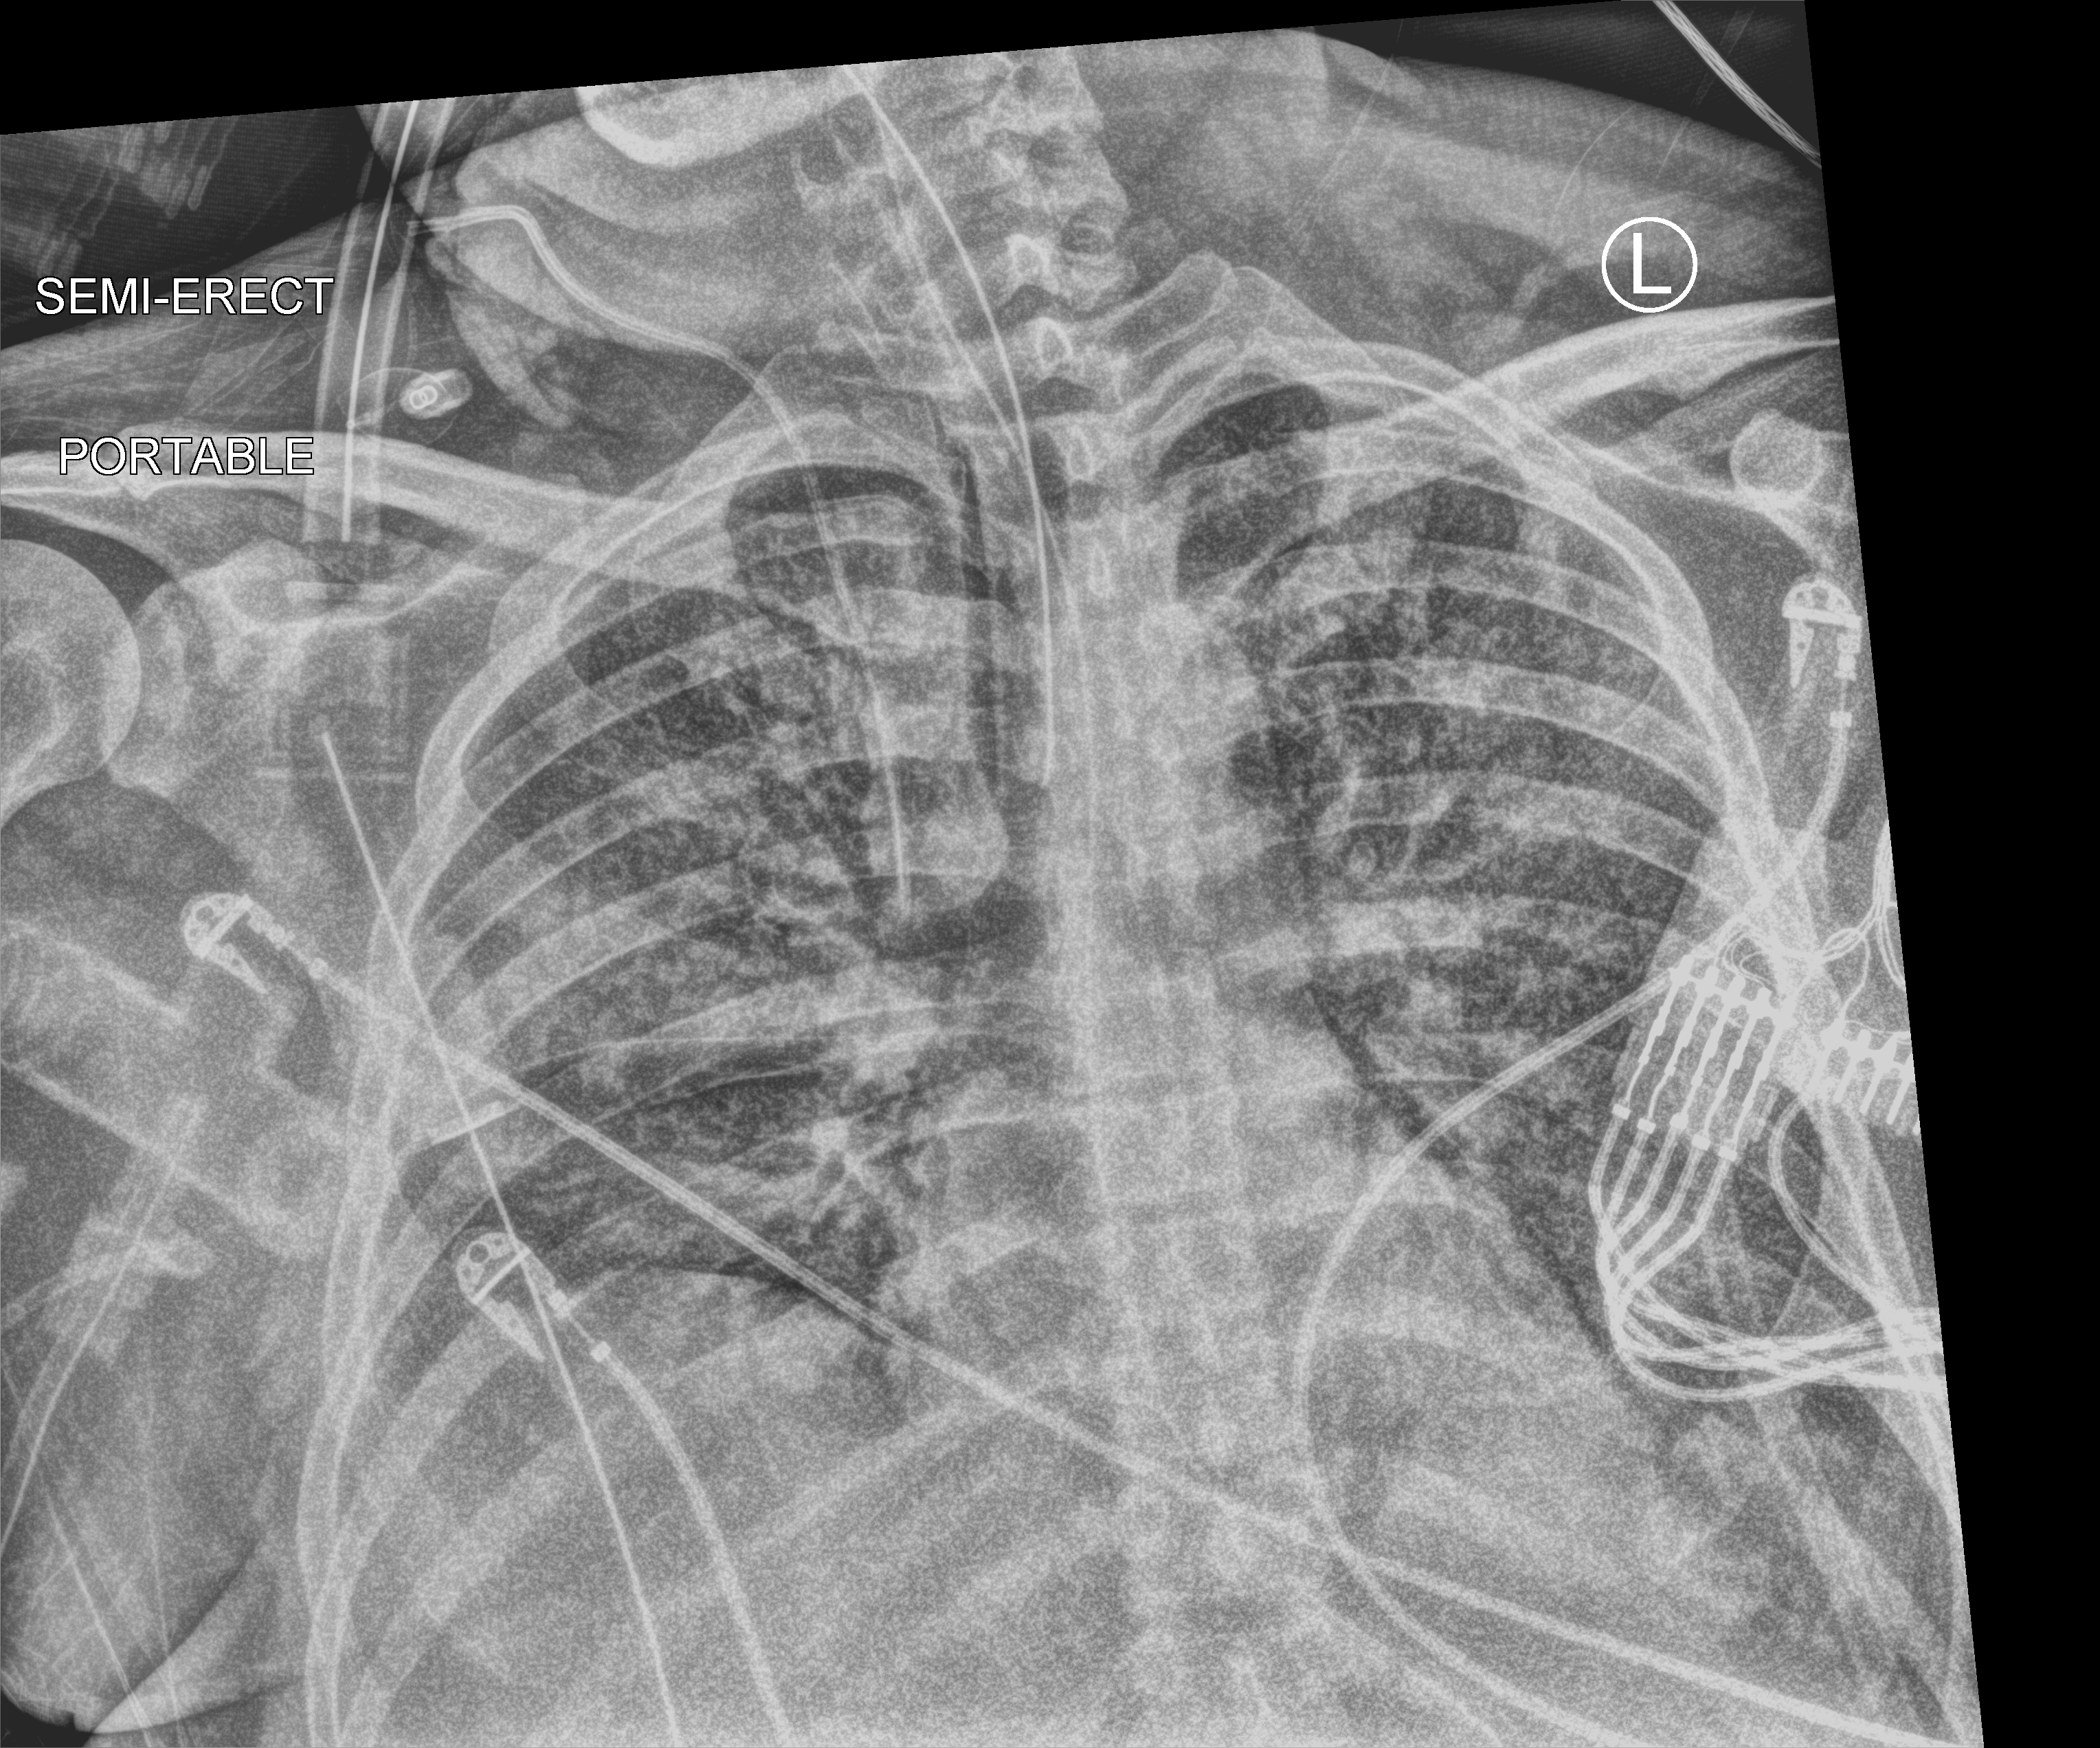
Chest X-ray (portable), anteroposterior (AP) projection. Male patient hospitalised with COVID-19, age 18–59 years.
Hospital-stay facts (about this admission, not read from this image; timing relative to this image not recorded): smoking status (admission record): never.